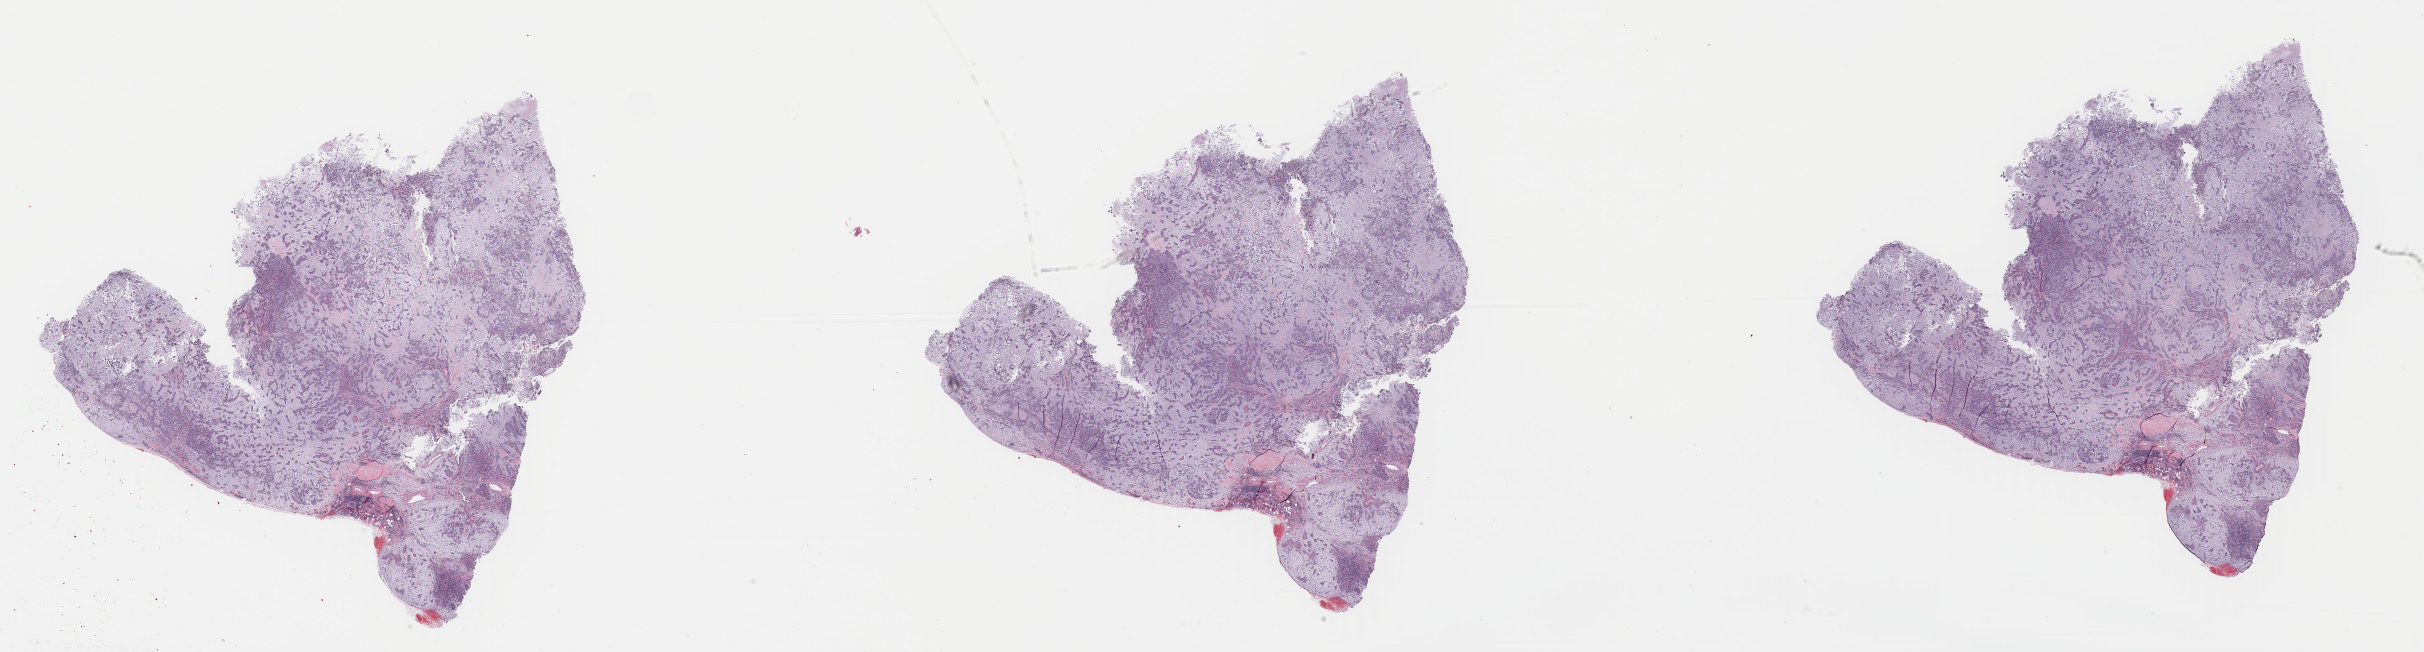
Digitized Hematoxylin and eosin (H&E) stained tissue section (whole slide), shown as a low-resolution overview of the whole scanned area (about 38.3 x 10.3 mm); formalin-fixed paraffin-embedded (FFPE) diagnostic section; head and neck, primary tumour sample. Female, age 48 years at initial diagnosis.
Pathologic diagnosis: Squamous cell carcinoma, NOS (larynx, NOS).